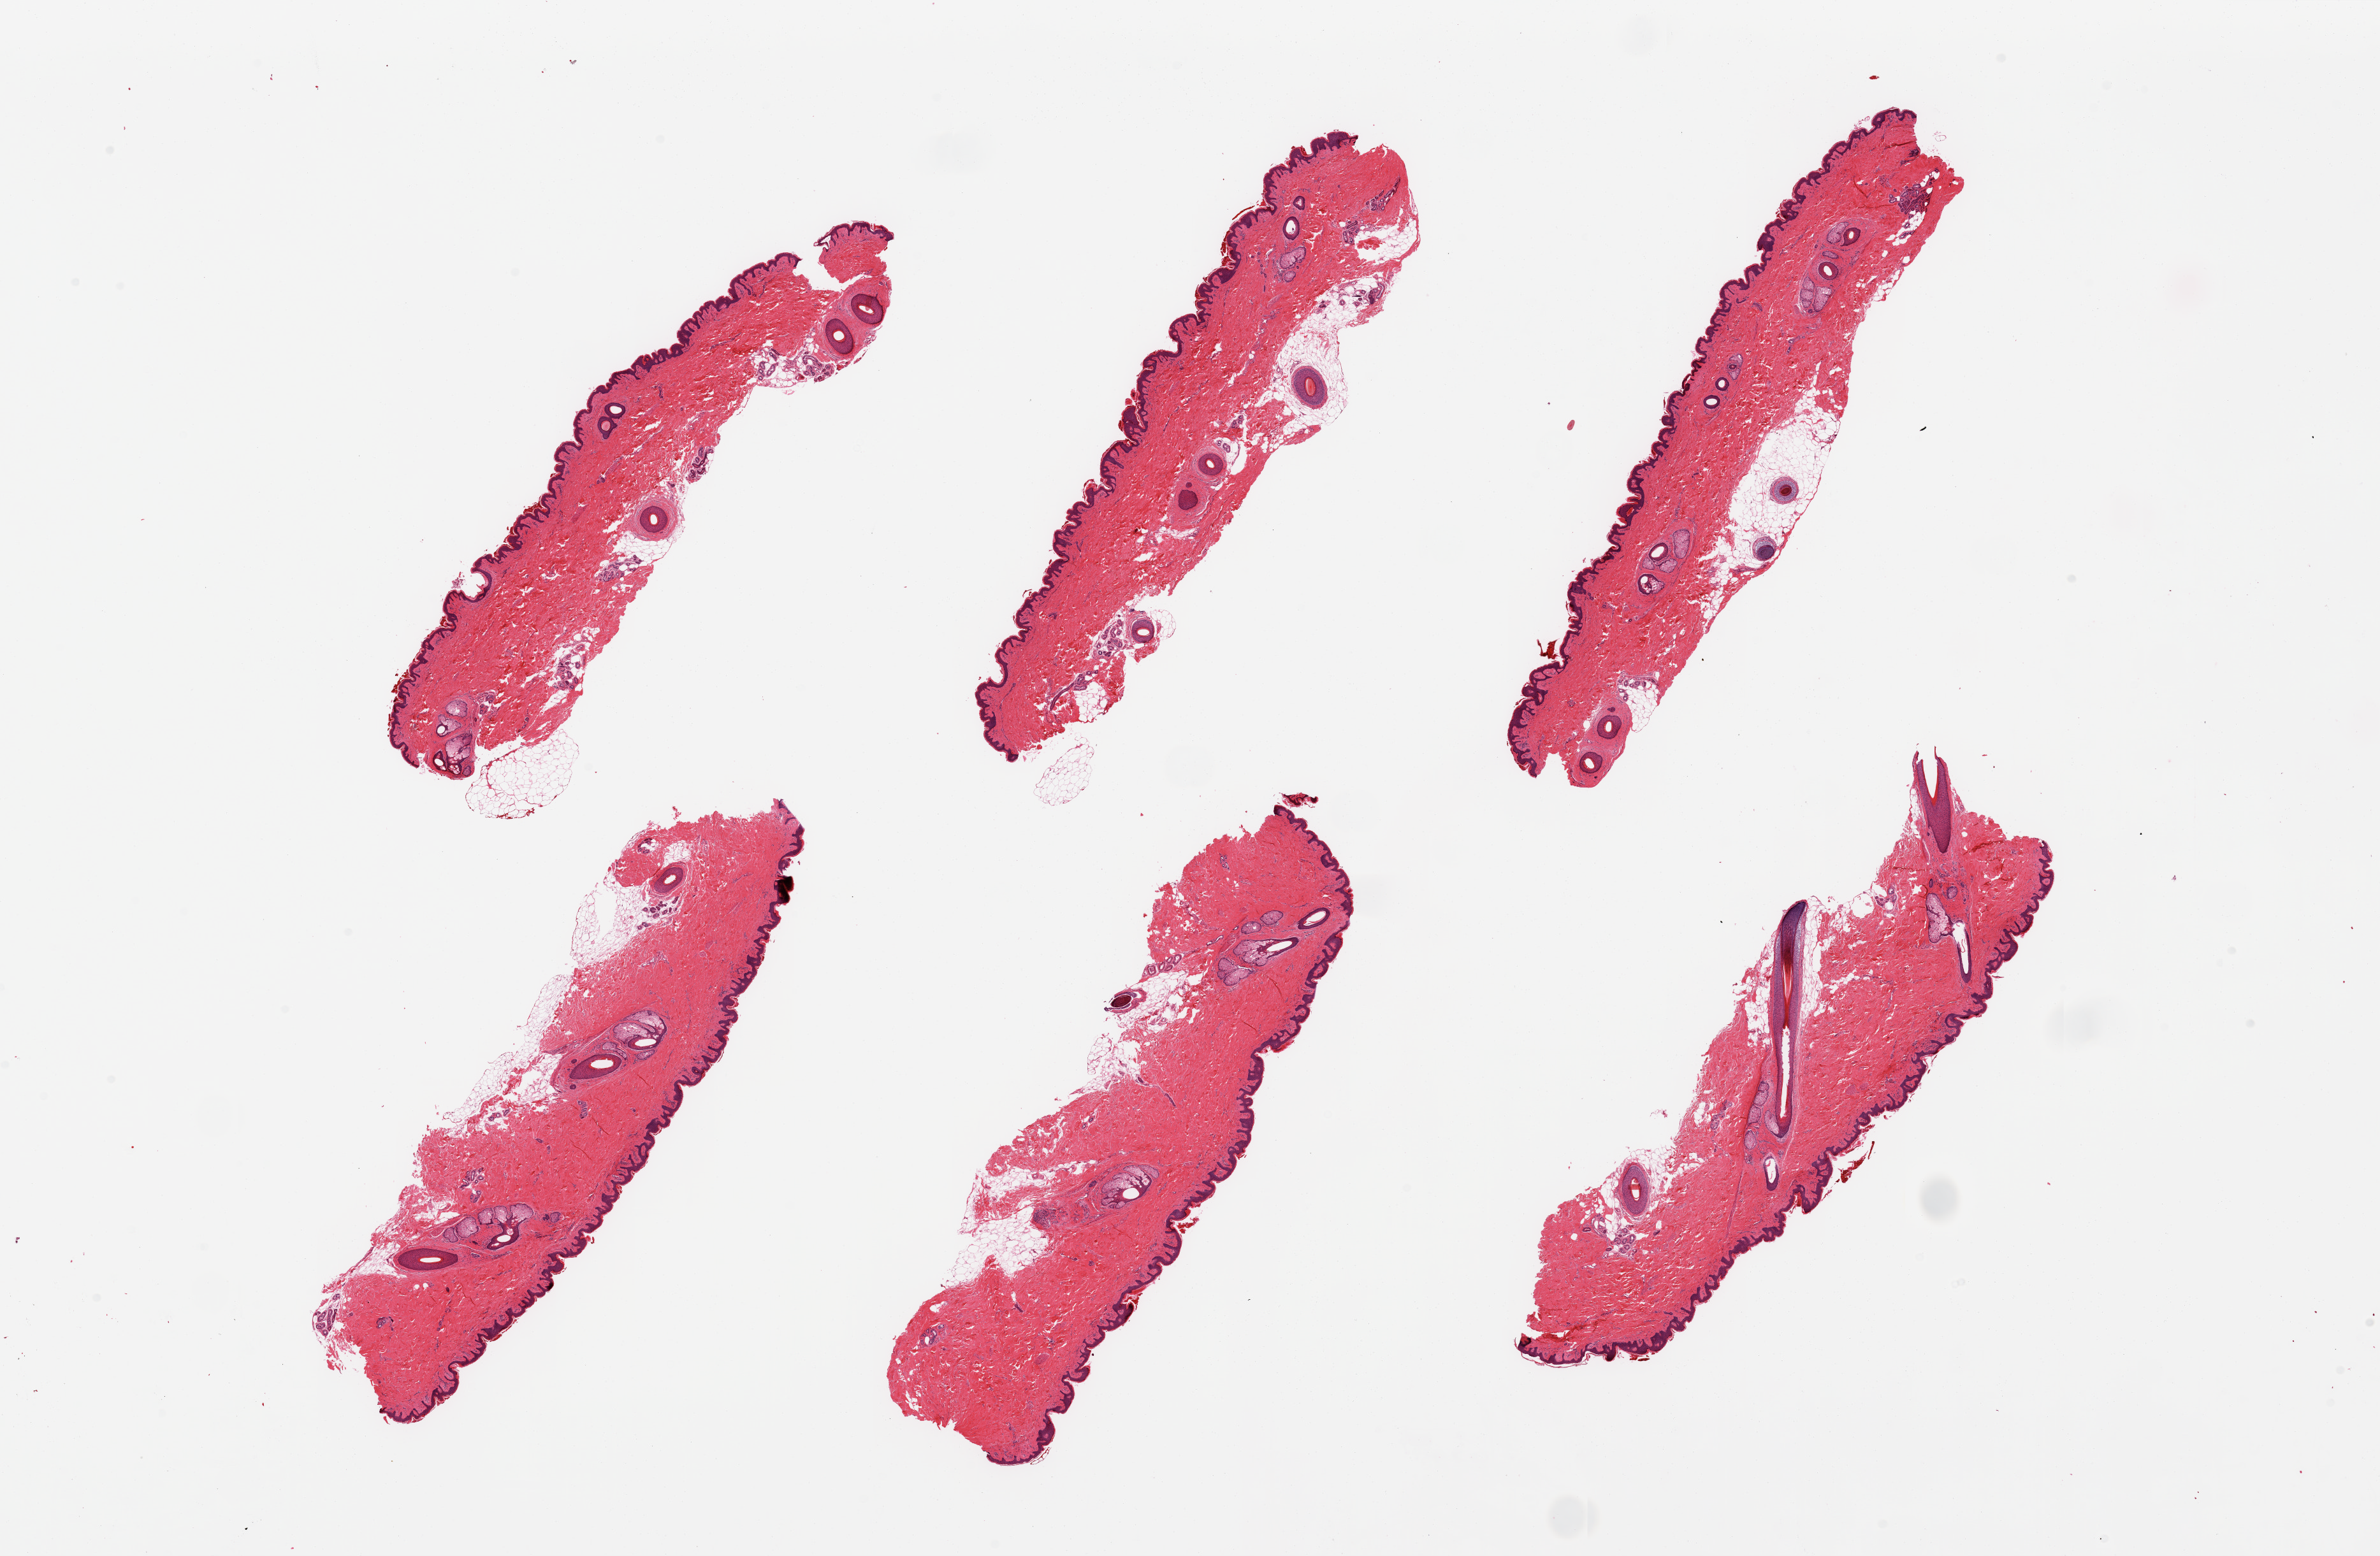
H&E whole-slide image, whole scanned area (about 29.5 x 19.3 mm) shown as a low-resolution overview, PAXgene-fixed paraffin-embedded (PFPE) section, sampled site (target tissue): skin of suprapubic region, donor tissue sample. Donor sex: male.
Pathologist's review note for this sample: 6 pieces; hair-bearing; 10% internal fat.